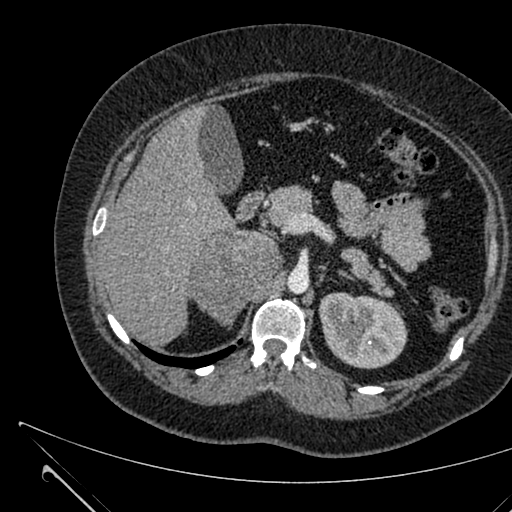
Contrast-enhanced abdominal CT, one axial slice; position 416 of 731 along the scan axis; intravenous contrast given; soft-tissue window (W 400 / L 40 HU); 1 mm slice thickness; 512 × 512 image matrix, field of view 376 × 376 mm. Patient: female, 36 years. From the clinical record (not read from this slice): diagnosis: adrenocortical carcinoma; tumour side: right adrenal; tumour size at pathology: 10 cm.
Outlined on this slice (semi-automatically segmented with operator editing):
- mass: box from (x=191, y=231) to (x=279, y=326) px